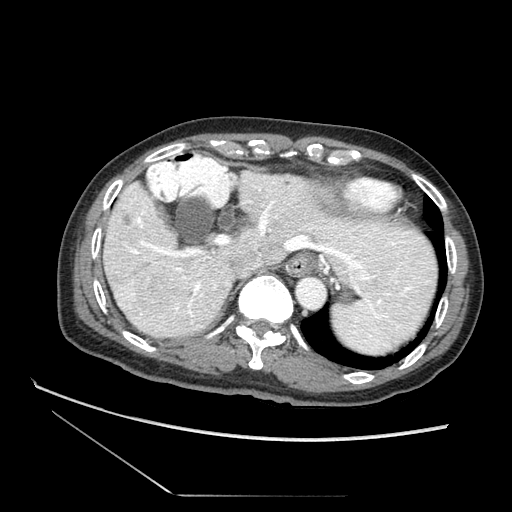
Contrast-enhanced abdominal CT (liver protocol), one axial slice; slice 59 of 73 in the series (ordered by position); reconstruction kernel STANDARD; 120 kVp; soft-tissue window (W 400 / L 40 HU); 512 × 512 image matrix. Case-level facts recorded for this patient, not image findings: diagnosis: hepatocellular carcinoma (patient treated with transarterial chemoembolisation; whether this scan precedes or follows treatment is not stated here); TNM stage (as recorded): Stage-II; Child-Pugh class: A.
Outlined on this slice (semi-automatic segmentation, software-assisted and operator-edited):
- liver parenchyma outside the tumour (the mass and vessels are separate outlines, so this box may not span the whole liver): bounding box [x1, y1, x2, y2] px = [104, 171, 443, 350]
- mass: [115, 265, 179, 318]
- liver vessels: [134, 188, 407, 282]